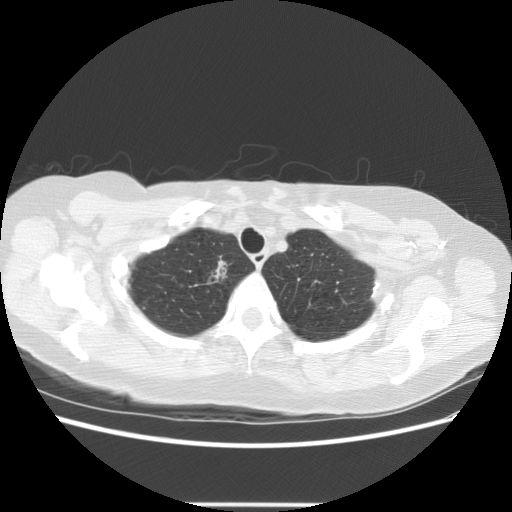
Low-dose screening chest CT, one axial slice. Position 109 of 126 along the scan axis. Reconstruction kernel STANDARD. 140 kVp. Lung window (W 1500 / L -600 HU). 2.5 mm slice thickness. 512 × 512 image matrix, field of view 360 × 360 mm.
Structures marked on this image (manually delineated by an expert):
- lesion 1 (tumor, upper lobe of right lung): bounding box <208,260,227,282> (left, top, right, bottom; pixels)